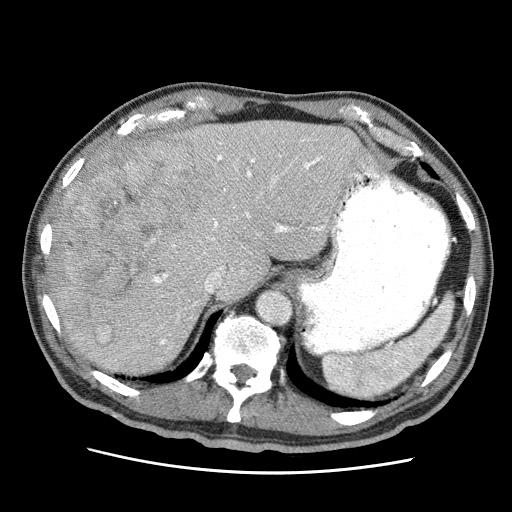
Contrast-enhanced abdominal CT (liver protocol), one axial slice. Position 45 of 75 along the scan axis. Reconstruction kernel STANDARD. Soft-tissue window (W 400 / L 40 HU). 2.5 mm slice thickness. 512 × 512 image matrix. Case-level facts recorded for this patient, not image findings: diagnosis: hepatocellular carcinoma (patient treated with transarterial chemoembolisation; whether this scan precedes or follows treatment is not stated here); TNM stage (as recorded): Stage-IIIA.
Structures marked on this image (semi-automatic segmentation, software-assisted and operator-edited):
- abdominal aorta: box from (x=257, y=290) to (x=291, y=324) px
- liver parenchyma outside the tumour (the mass and vessels are separate outlines, so this box may not span the whole liver): (x=52, y=120)–(x=376, y=374)
- mass: (x=0, y=139)–(x=215, y=512)
- liver vessels: (x=152, y=133)–(x=373, y=348)